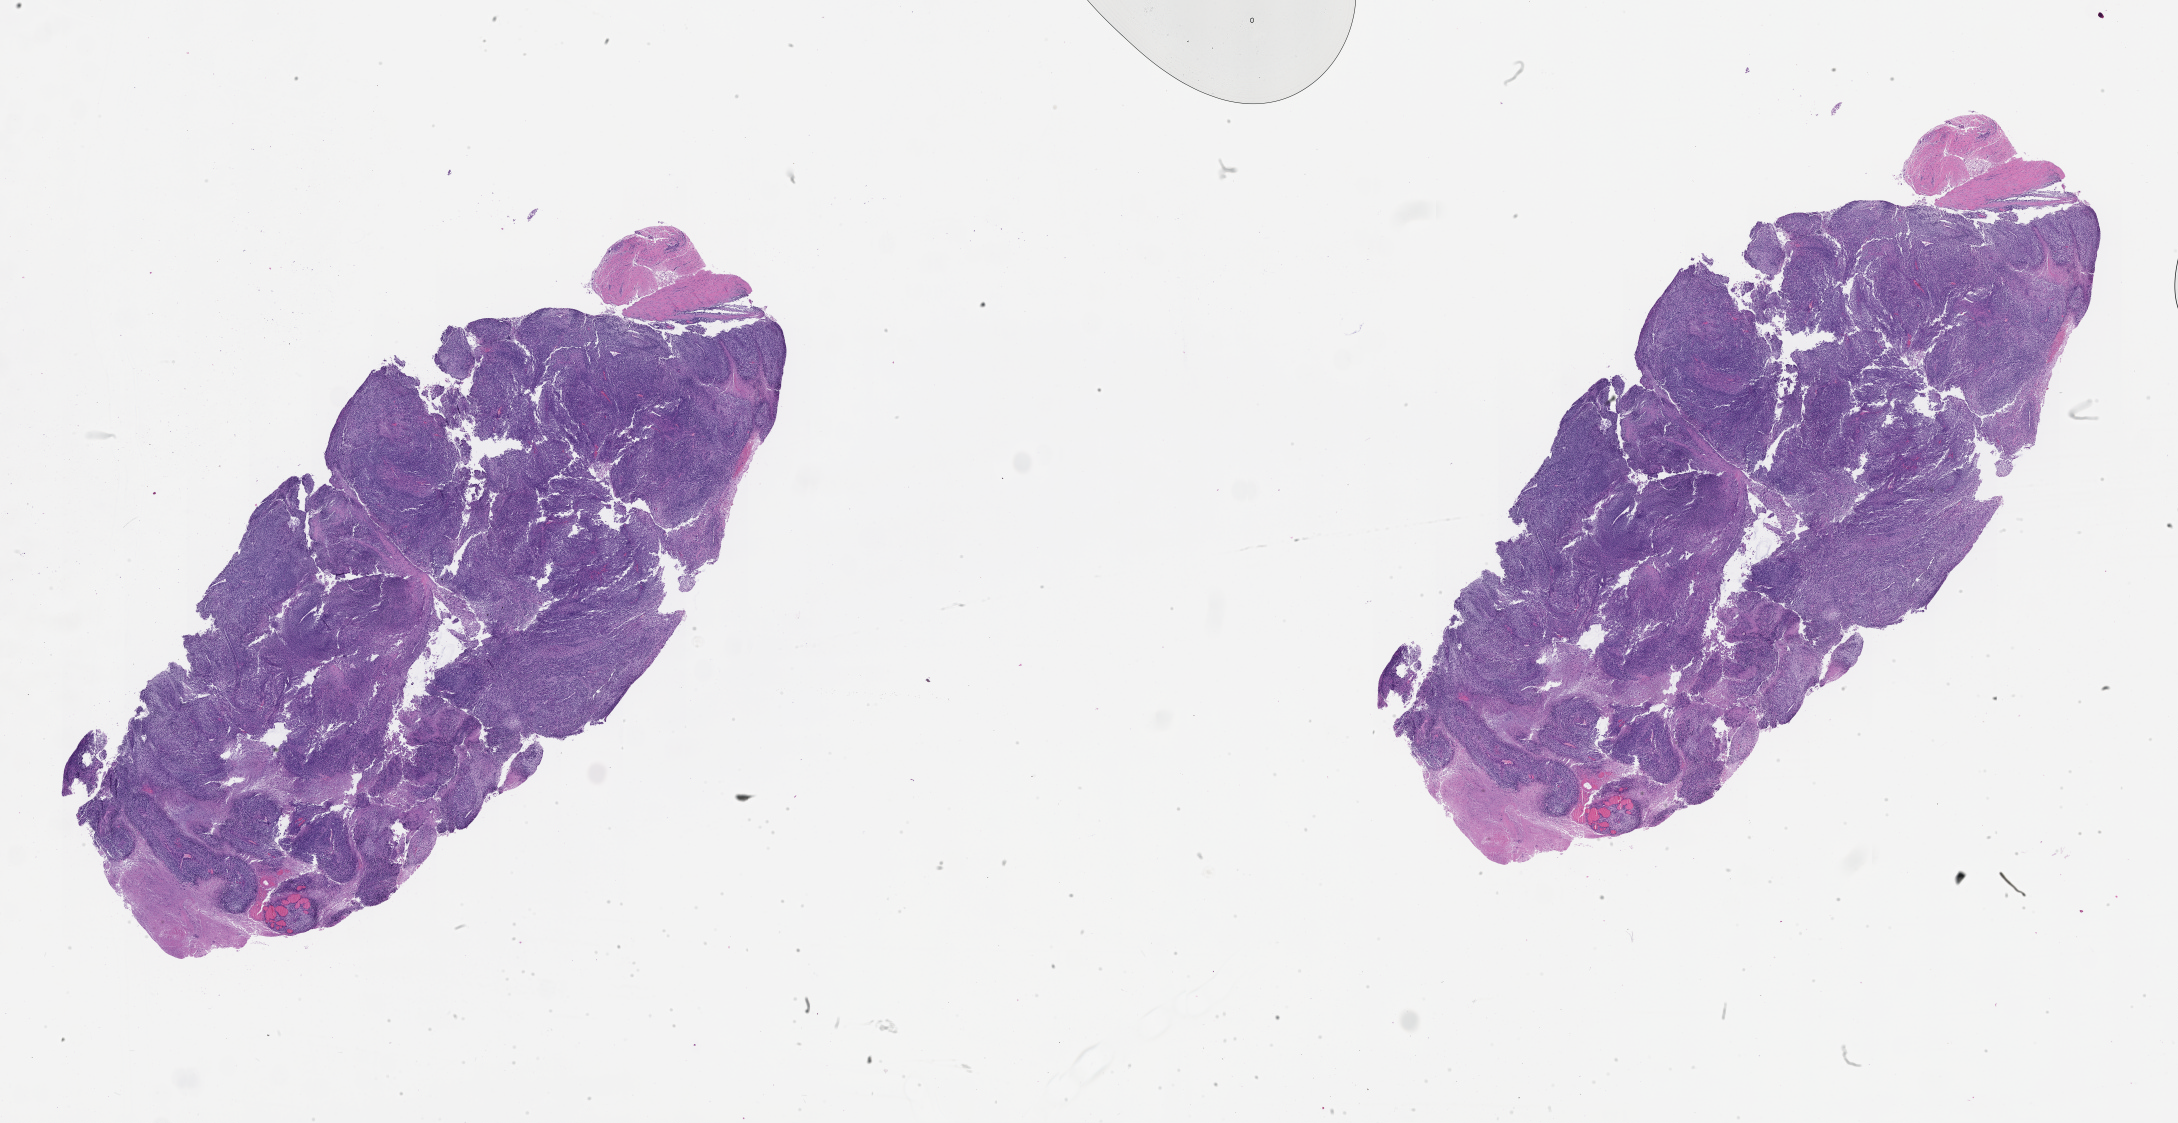
Digitized Hematoxylin and eosin (H&E) stained tissue section (whole slide) — a low-resolution overview of the entire scanned area, about 35.1 x 18.1 mm.
Patient diagnosis (cohort enrolment): sarcoma (site not recorded at cohort level).